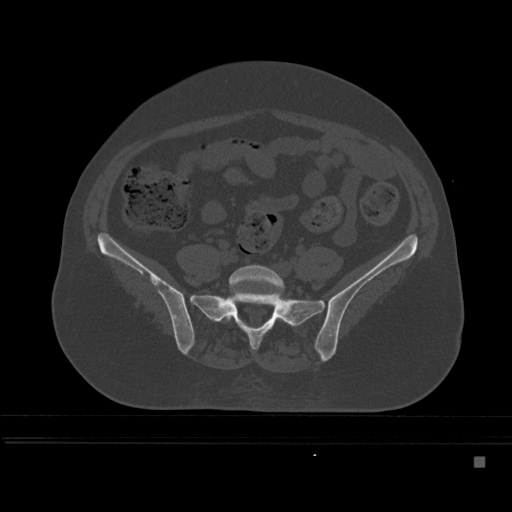
CT including the spine, one axial slice; position 99 of 495 along the scan axis; bone window (W 1800 / L 400 HU); 1.5 mm slice thickness; 512 × 512 image matrix. Female patient, age 33 years. Case-level facts recorded for this patient, not image findings: primary cancer: breast; vertebrae with lytic lesions (as recorded): T1.
Structures marked on this image (semi-automatically segmented with operator editing):
- L5 vertebra: bounding box <218,265,285,322> (left, top, right, bottom; pixels)